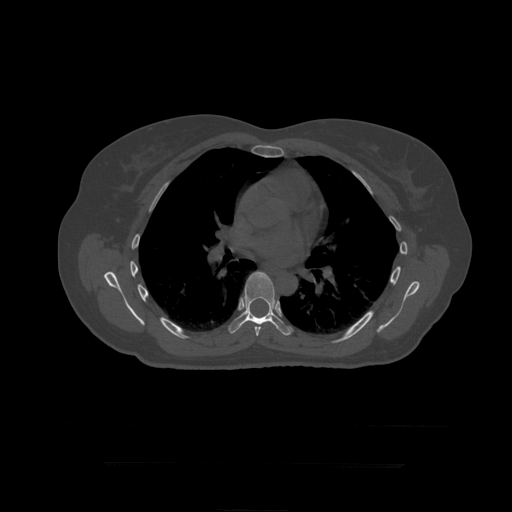
CT including the spine, one axial slice. Reconstruction kernel STANDARD. 120 kVp. Bone window (W 1800 / L 400 HU). 512 × 512 image matrix. Patient age 41 years. Case-level facts recorded for this patient, not image findings: primary cancer: breast.
Outlined on this slice (semi-automatically segmented with operator editing):
- T7 vertebra: box from (x=255, y=326) to (x=262, y=336) px
- T8 vertebra: (x=228, y=272)–(x=292, y=336)